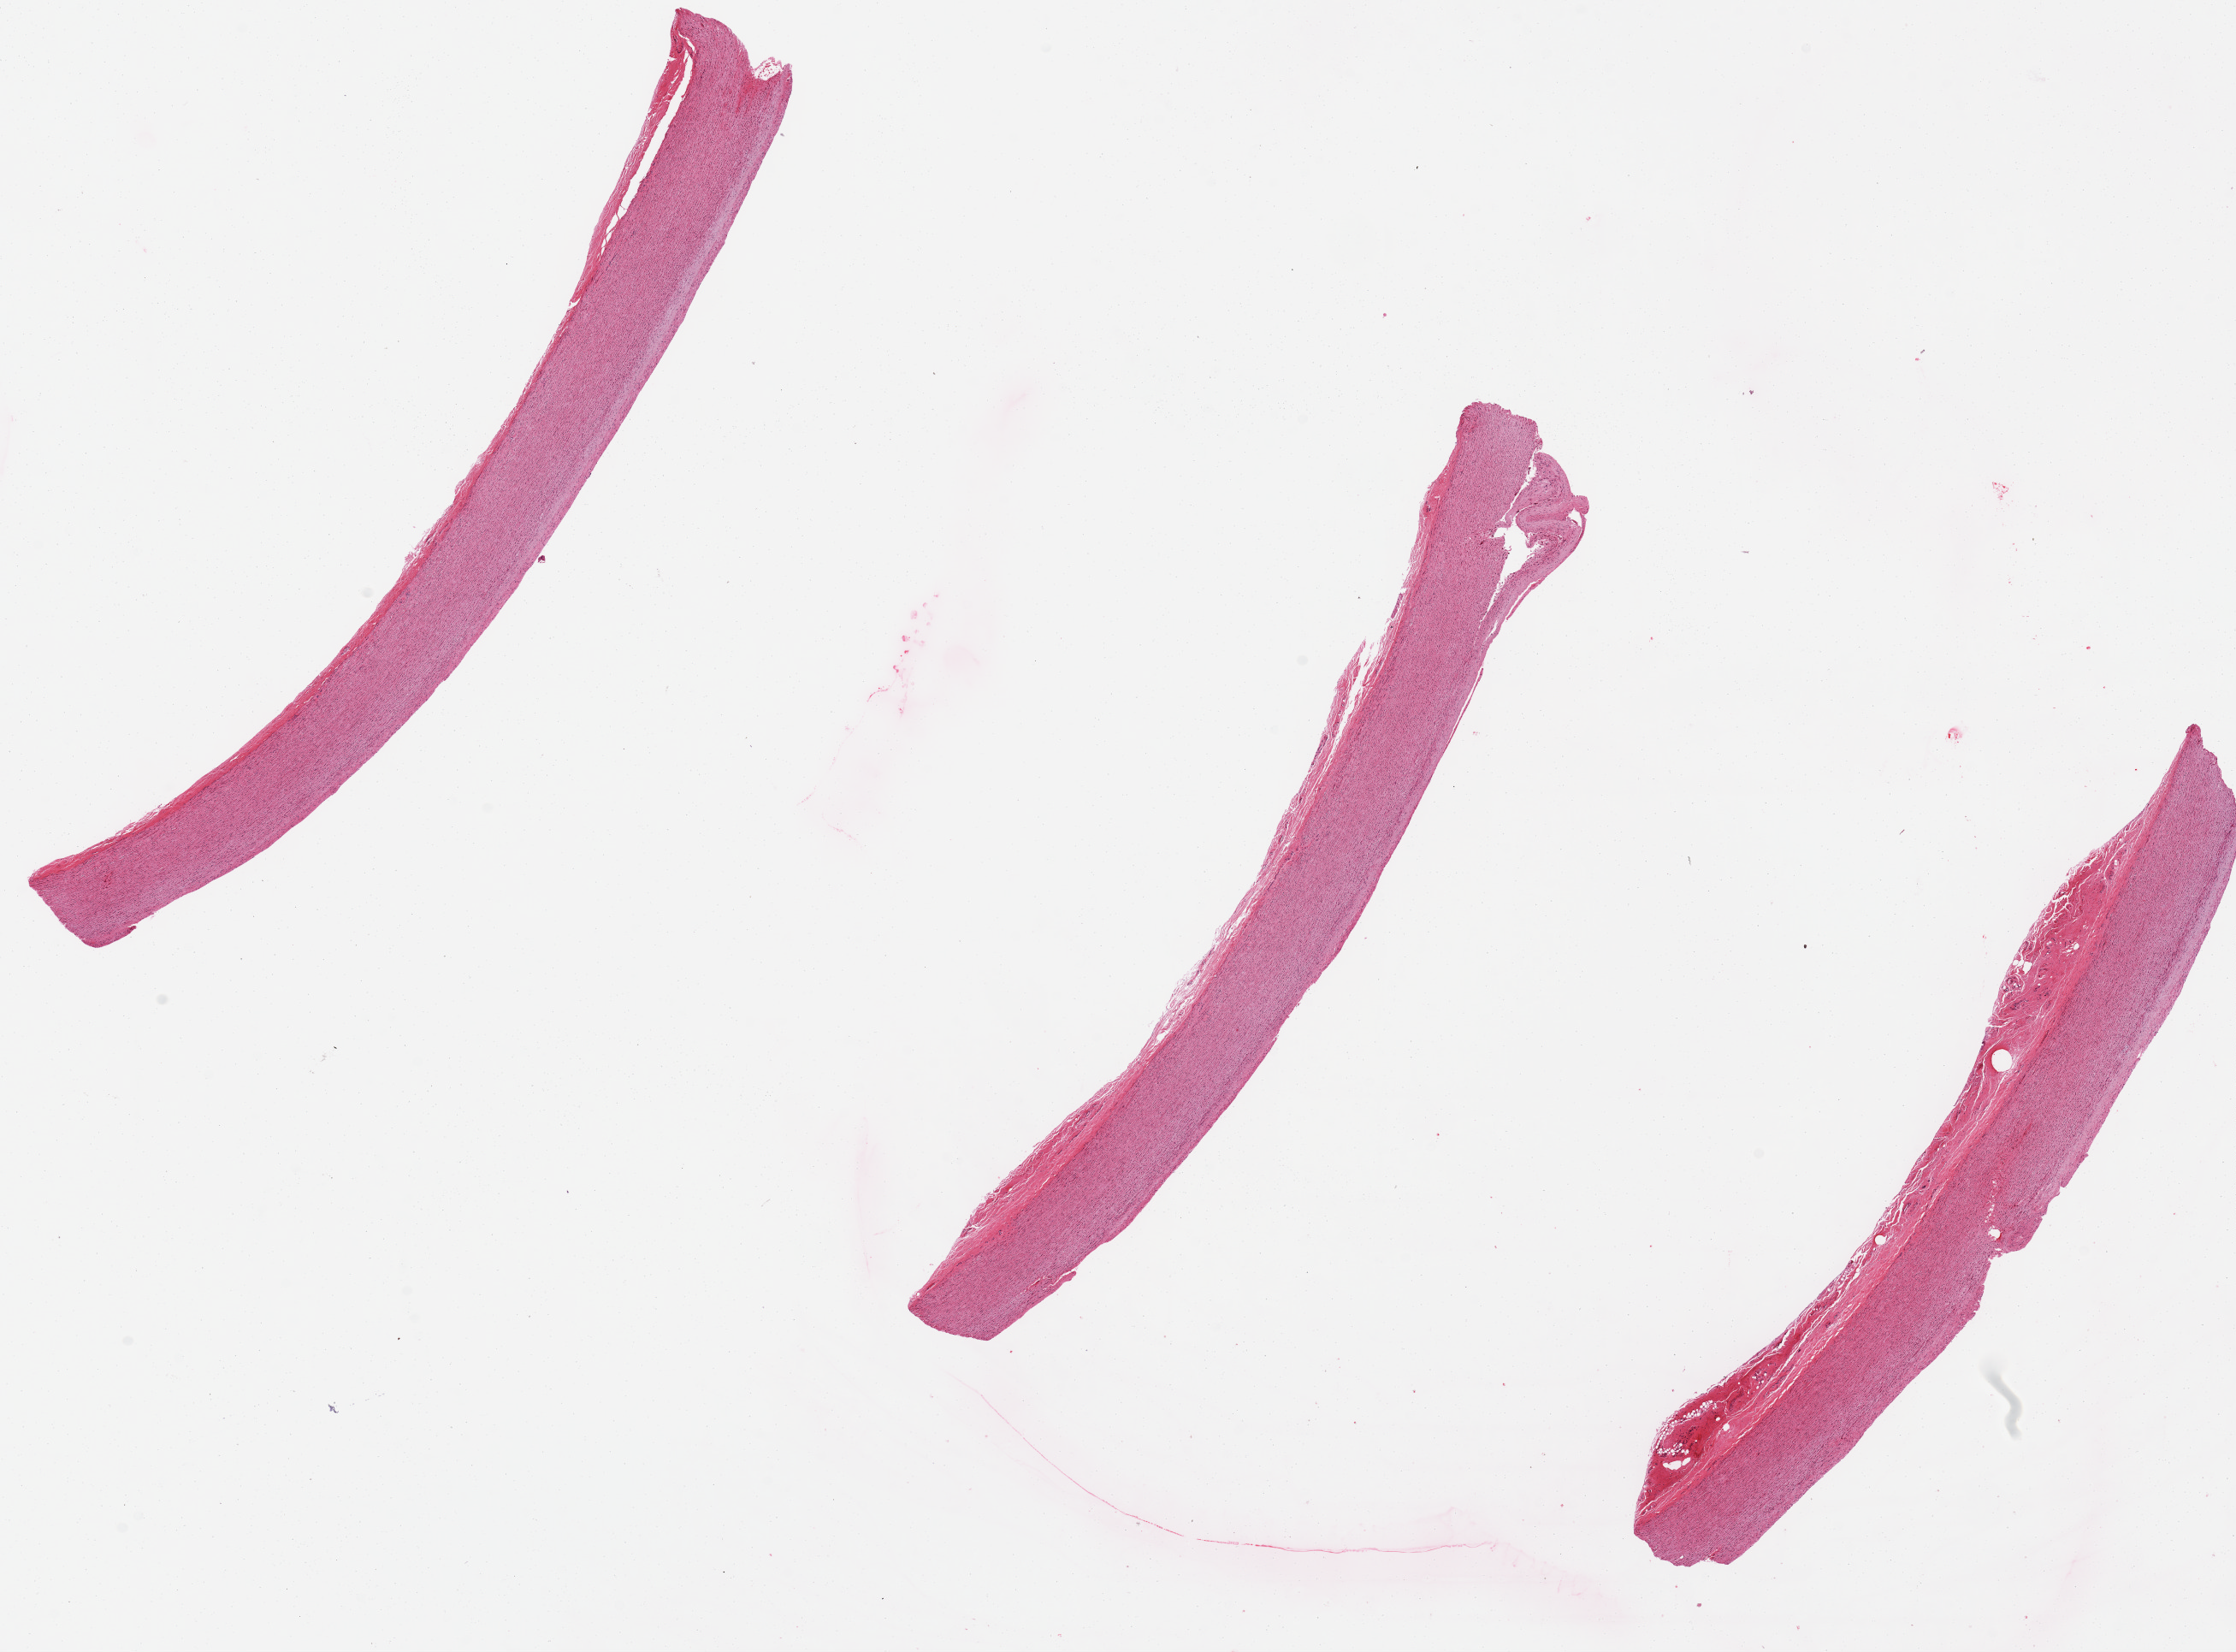
H&E whole-slide image — shown as a low-resolution overview of the whole scanned area (about 20.7 x 15.3 mm, from a 20x scan), PAXgene-fixed, paraffin-embedded tissue, sampled site (target tissue): aorta, tissue donor sample.
Reviewer comment on this tissue sample: 3 pieces, 10x1mm specimens.